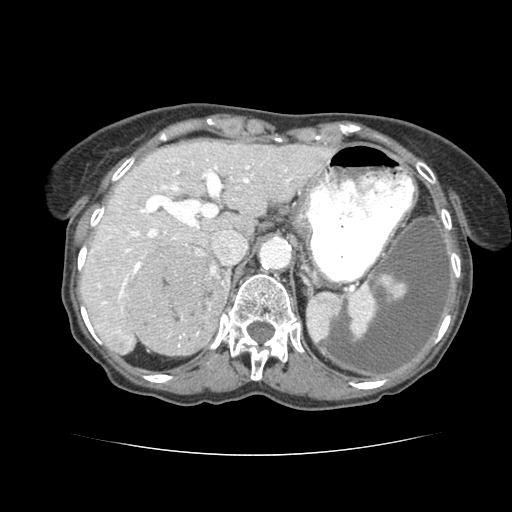
Contrast-enhanced abdominal CT (liver protocol), one axial slice; slice 53 of 77 in the series (ordered by position); reconstruction kernel STANDARD; 120 kVp; soft-tissue window (W 400 / L 40 HU); 2.5 mm slice thickness; 512 × 512 image matrix. Case-level facts recorded for this patient, not image findings: diagnosis: hepatocellular carcinoma (patient treated with transarterial chemoembolisation; whether this scan precedes or follows treatment is not stated here); TNM stage (as recorded): Stage-I; Child-Pugh class: A; tumour differentiation: well differentiated; tumour size: 7.6 cm.
Outlined on this slice (semi-automatic segmentation, software-assisted and operator-edited):
- liver parenchyma outside the tumour (the mass and vessels are separate outlines, so this box may not span the whole liver): bounding box [x1, y1, x2, y2] px = [76, 136, 324, 352]
- mass: [128, 241, 226, 355]
- liver vessels: [96, 159, 321, 308]